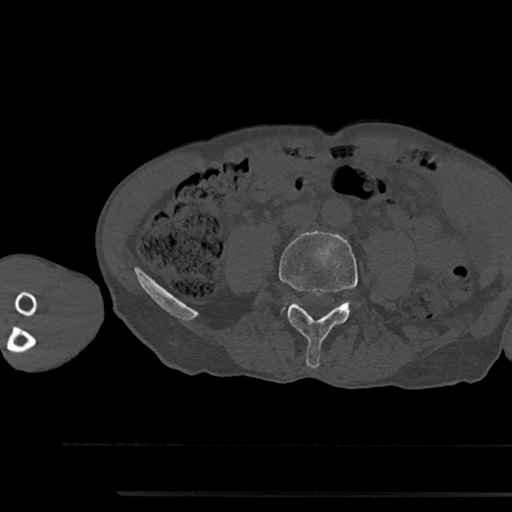
CT including the spine, one axial slice; slice 402 of 797 in the series (ordered by position); reconstruction kernel Br40s/3; 120 kVp; bone window (W 1800 / L 400 HU); 0.5 mm slice thickness; 512 × 512 image matrix, field of view 367 × 367 mm. Male patient, age 79 years. From the clinical record (not read from this slice): primary cancer: prostate.
Annotated regions visible in this slice (semi-automatically segmented with operator editing):
- L4 vertebra: bounding box [x1, y1, x2, y2] px = [279, 231, 358, 368]